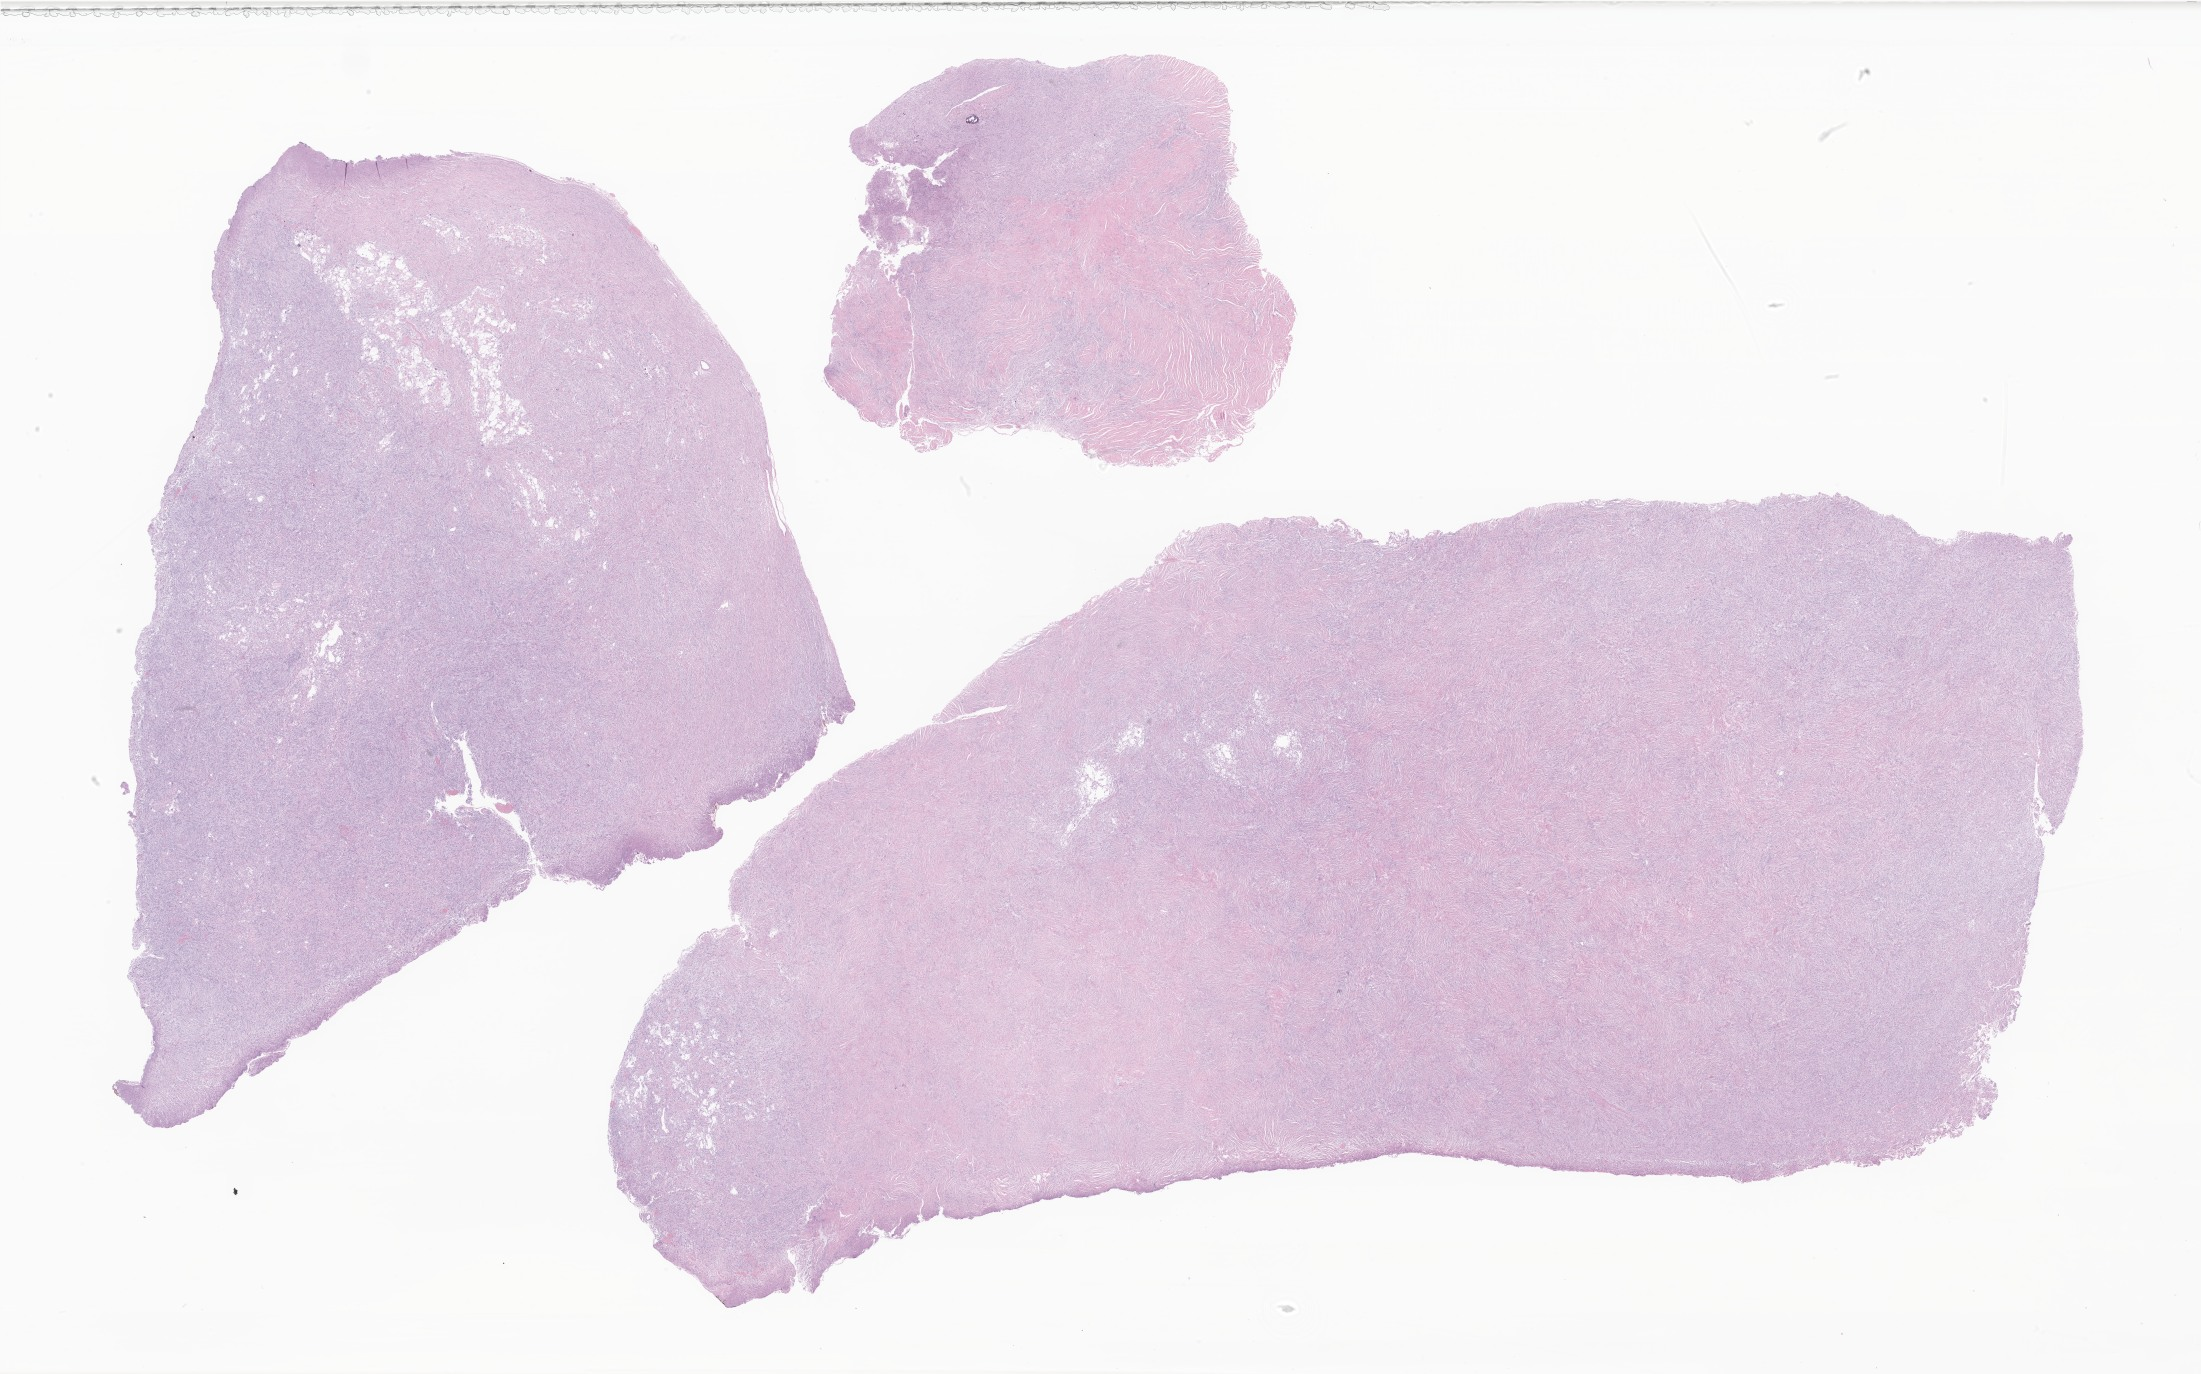
Whole-slide image, haematoxylin and eosin stain of tumor tissue from the brain, low-resolution overview of the scanned area, about 37.1 x 23.2 mm; FFPE section. Patient male; age 37 months.
Diagnosis: Neoplasm, uncertain whether benign or malignant.